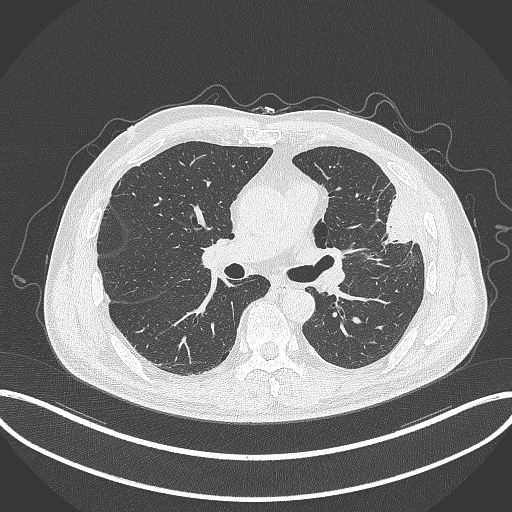
Chest CT, one axial slice; position 188 of 382 along the scan axis; reconstruction kernel B70f; lung window (W 1500 / L -600 HU); 1 mm slice thickness; 512 × 512 image matrix. Male patient, age 64 years. Case-level facts recorded for this patient, not image findings: clinical TNM (as recorded): T4 N1 M0.
Structures marked on this image (bounding box drawn by a radiologist):
- lung tumour (recorded histology: adenocarcinoma): box from (x=371, y=193) to (x=422, y=246) px